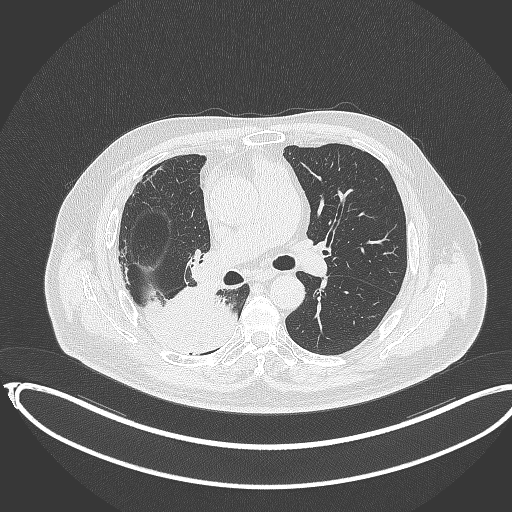
Chest CT, one axial slice; position 204 of 403 along the scan axis; 120 kVp; lung window (W 1500 / L -600 HU); 1 mm slice thickness; 512 × 512 image matrix, field of view 436 × 436 mm. Patient: male, 68 years. Case-level facts recorded for this patient, not image findings: clinical TNM (as recorded): T2a N0 M0.
Annotated regions visible in this slice (rectangle marked by the reading radiologist):
- lung tumour (recorded histology: adenocarcinoma): bounding box <141,283,244,365> (left, top, right, bottom; pixels)